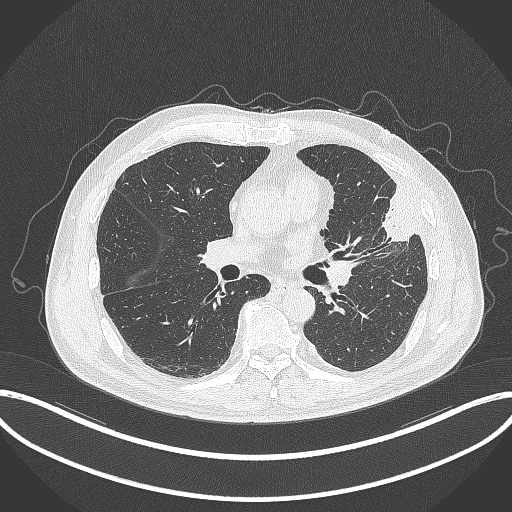
Chest CT, one axial slice; lung window (W 1500 / L -600 HU); 512 × 512 image matrix, field of view 415 × 415 mm. Male patient, age 64 years. Case-level facts recorded for this patient, not image findings: clinical TNM (as recorded): T4 N1 M0.
Outlined on this slice (bounding box drawn by a radiologist):
- lung tumour (recorded histology: adenocarcinoma): box from (x=374, y=184) to (x=422, y=244) px